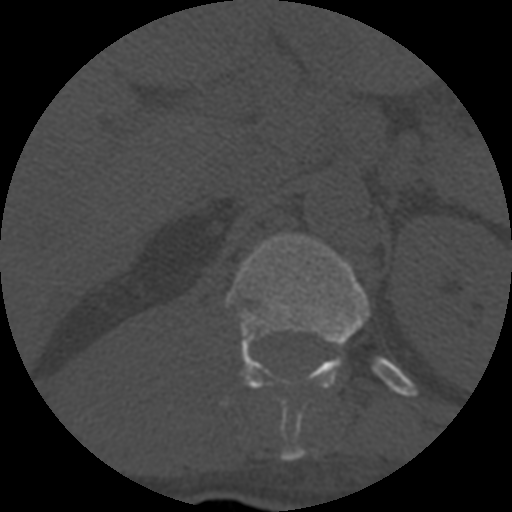
CT including the spine, one axial slice; slice 310 of 708 in the series (ordered by position); one of 3 acquisitions stored at this slice position; bone window (W 1800 / L 400 HU); 1.25 mm slice thickness; 512 × 512 image matrix, field of view 160 × 160 mm. Patient age 55 years. From the clinical record (not read from this slice): primary cancer: colon; vertebrae with lytic lesions (as recorded): T12, L1, L5.
Outlined on this slice (semi-automatic segmentation, software-assisted and operator-edited):
- T12 vertebra: bounding box <226,233,370,462> (left, top, right, bottom; pixels)